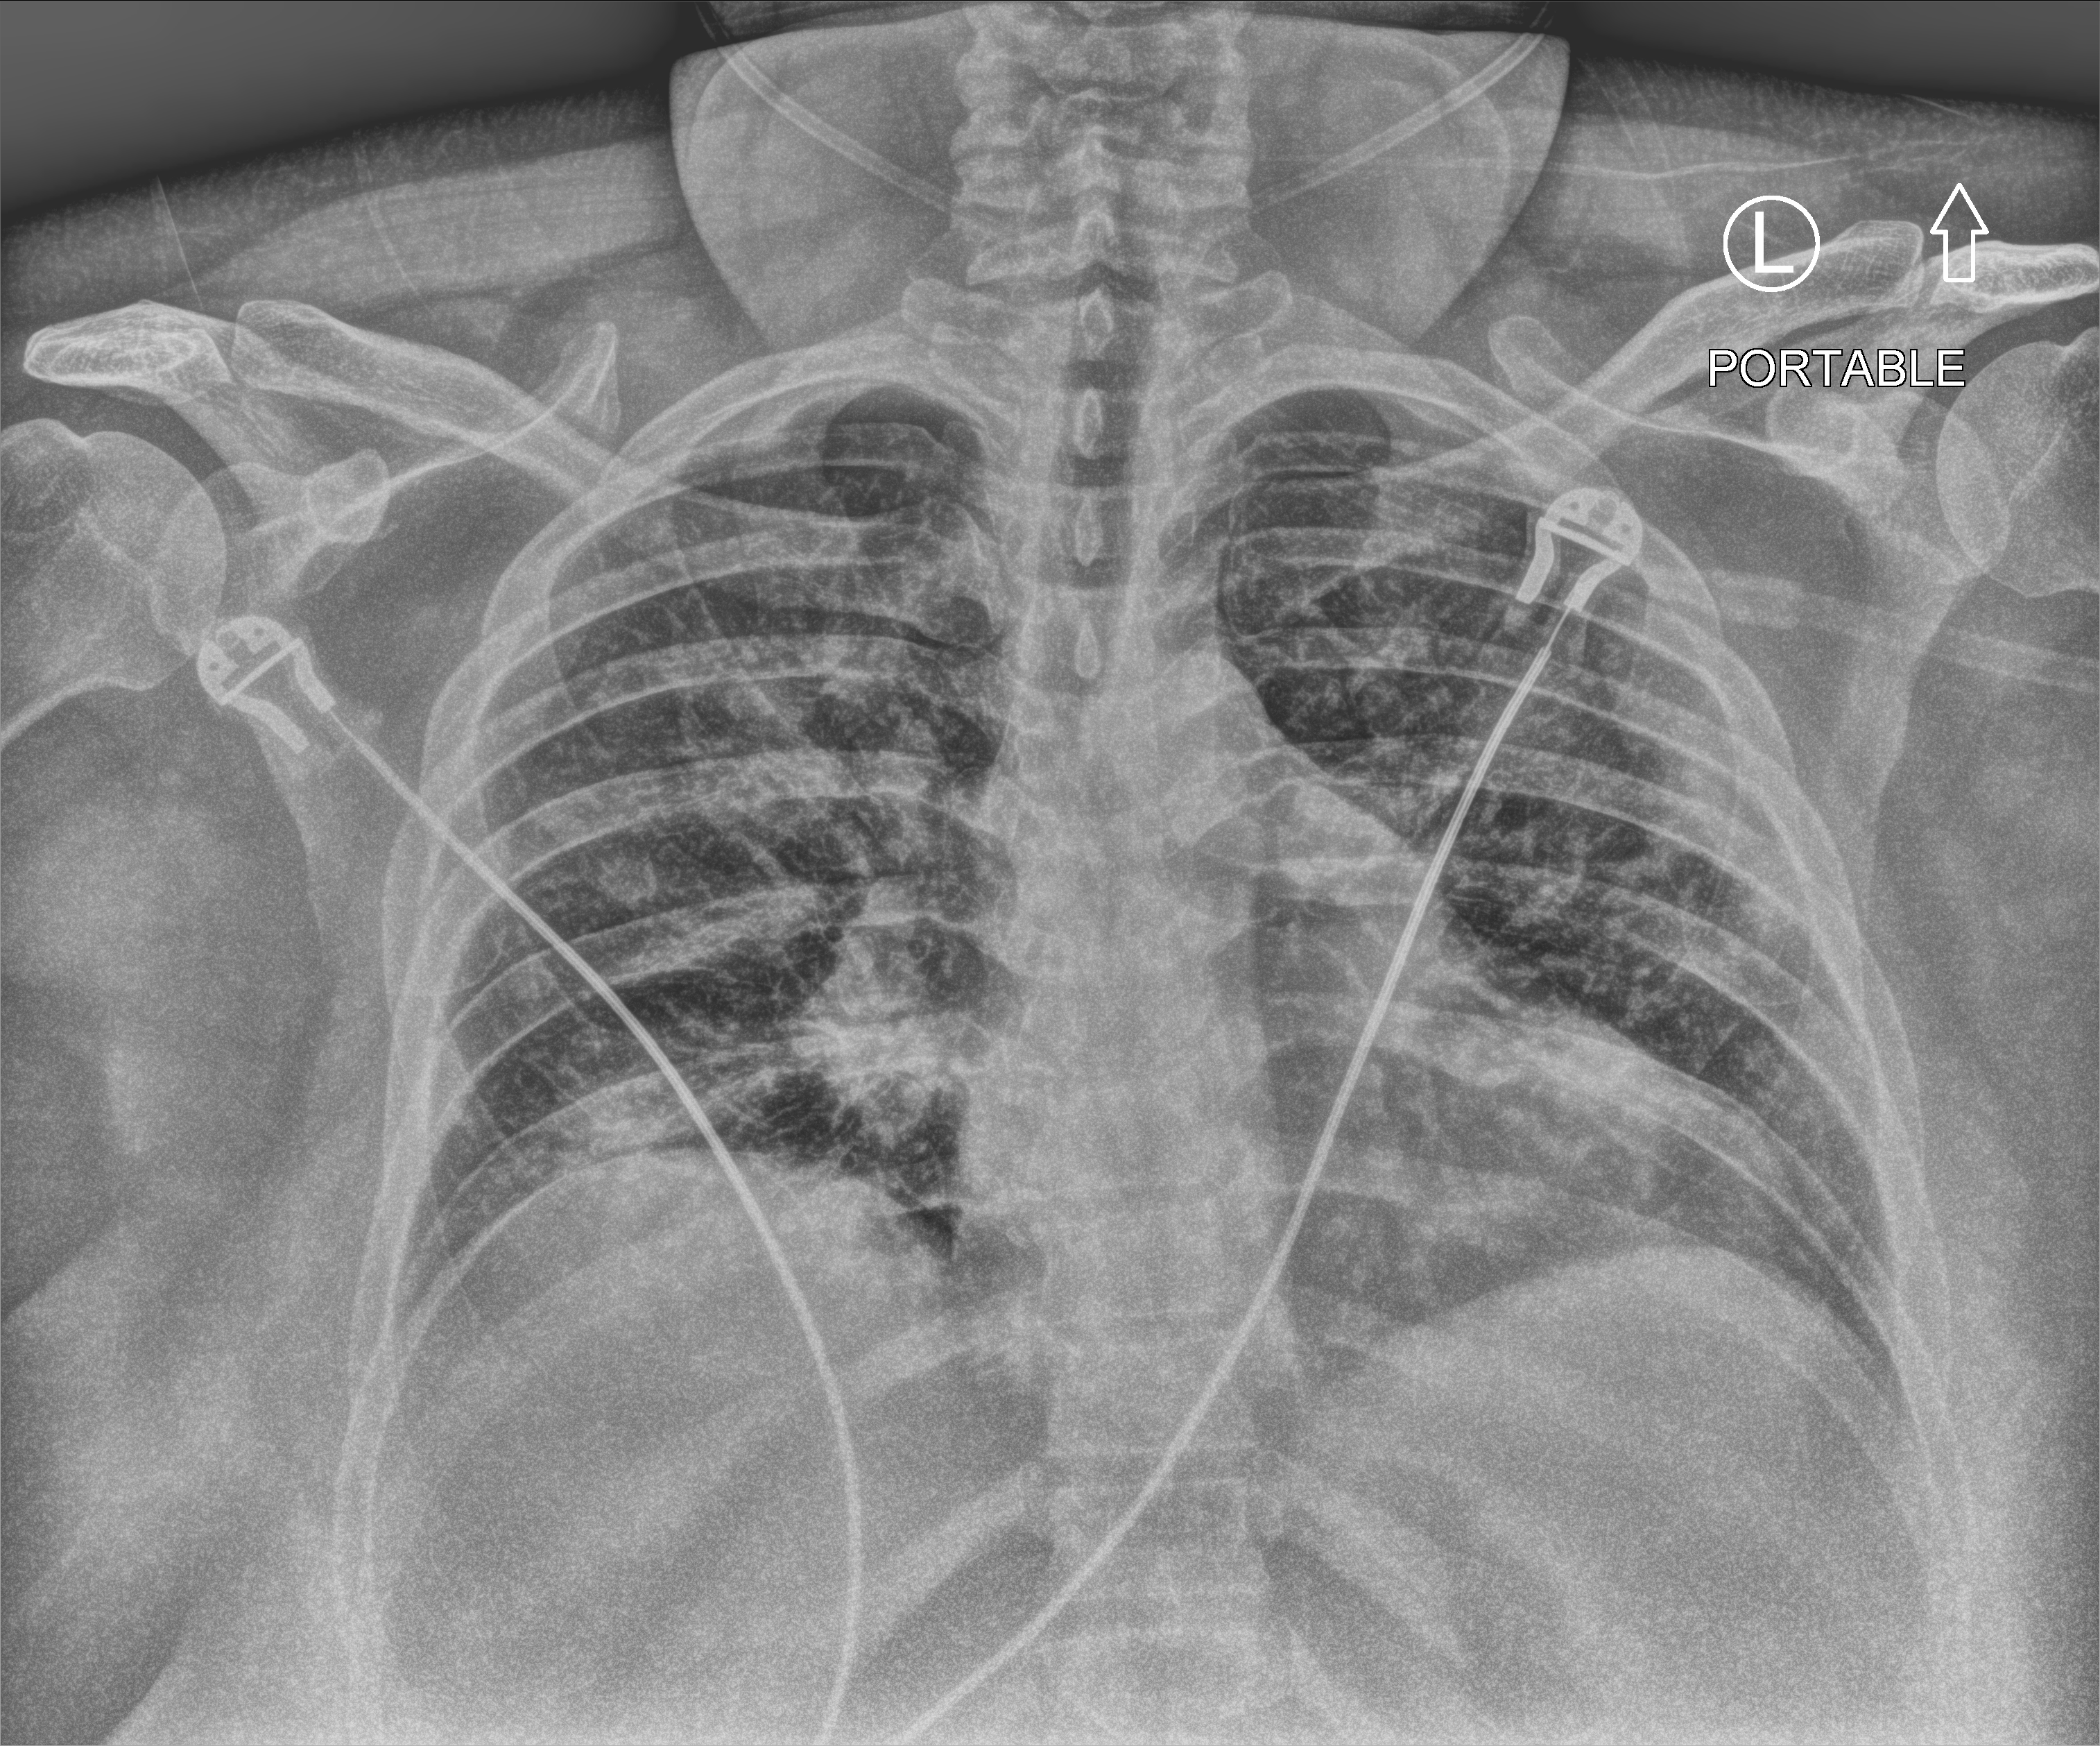
Bedside chest radiograph (computed radiography); anteroposterior (AP) projection. Patient hospitalised with COVID-19; female, aged 18–59 years.
From the hospital-stay record, not from the radiograph (when in the stay this image was taken is not recorded):
- admitted to intensive care during this hospital stay: no
- mechanically ventilated during this hospital stay: no